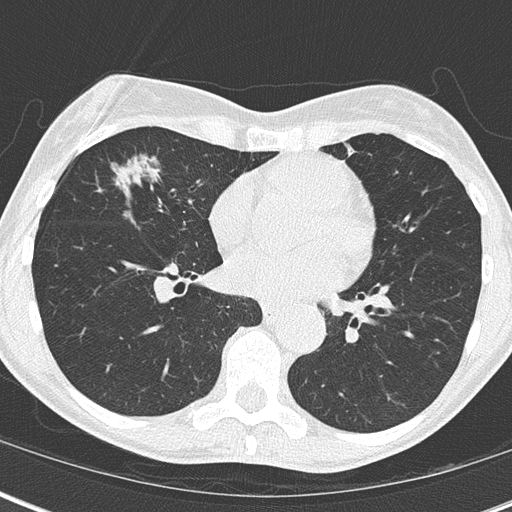
Low-dose screening chest CT, axial slice. Third screening round (two years after baseline). Lung window (W 1500 / L -600 HU). 2 mm slice thickness. Lung (sharp) reconstruction kernel (B50f). 512 × 512 image matrix, field of view 290 × 290 mm. Female, age 67 years at enrolment. Current smoker at enrolment.
Expert-annotated lung lesion, box from (x=95, y=146) to (x=197, y=243) px. Screening reader's record for this exam (one nodule recorded; not confirmed to be the boxed lesion): non-calcified nodule or mass ≥4 mm, right middle lobe, 32 × 17 mm, mixed attenuation, pre-existing on the prior screen: yes; interval growth: yes. Later outcome: lung cancer diagnosed 76 days after this screen — bronchiolo-alveolar adenocarcinoma, NOS, right middle lobe, well differentiated (G1), stage IA (AJCC 6th edition), 25 mm at pathology.